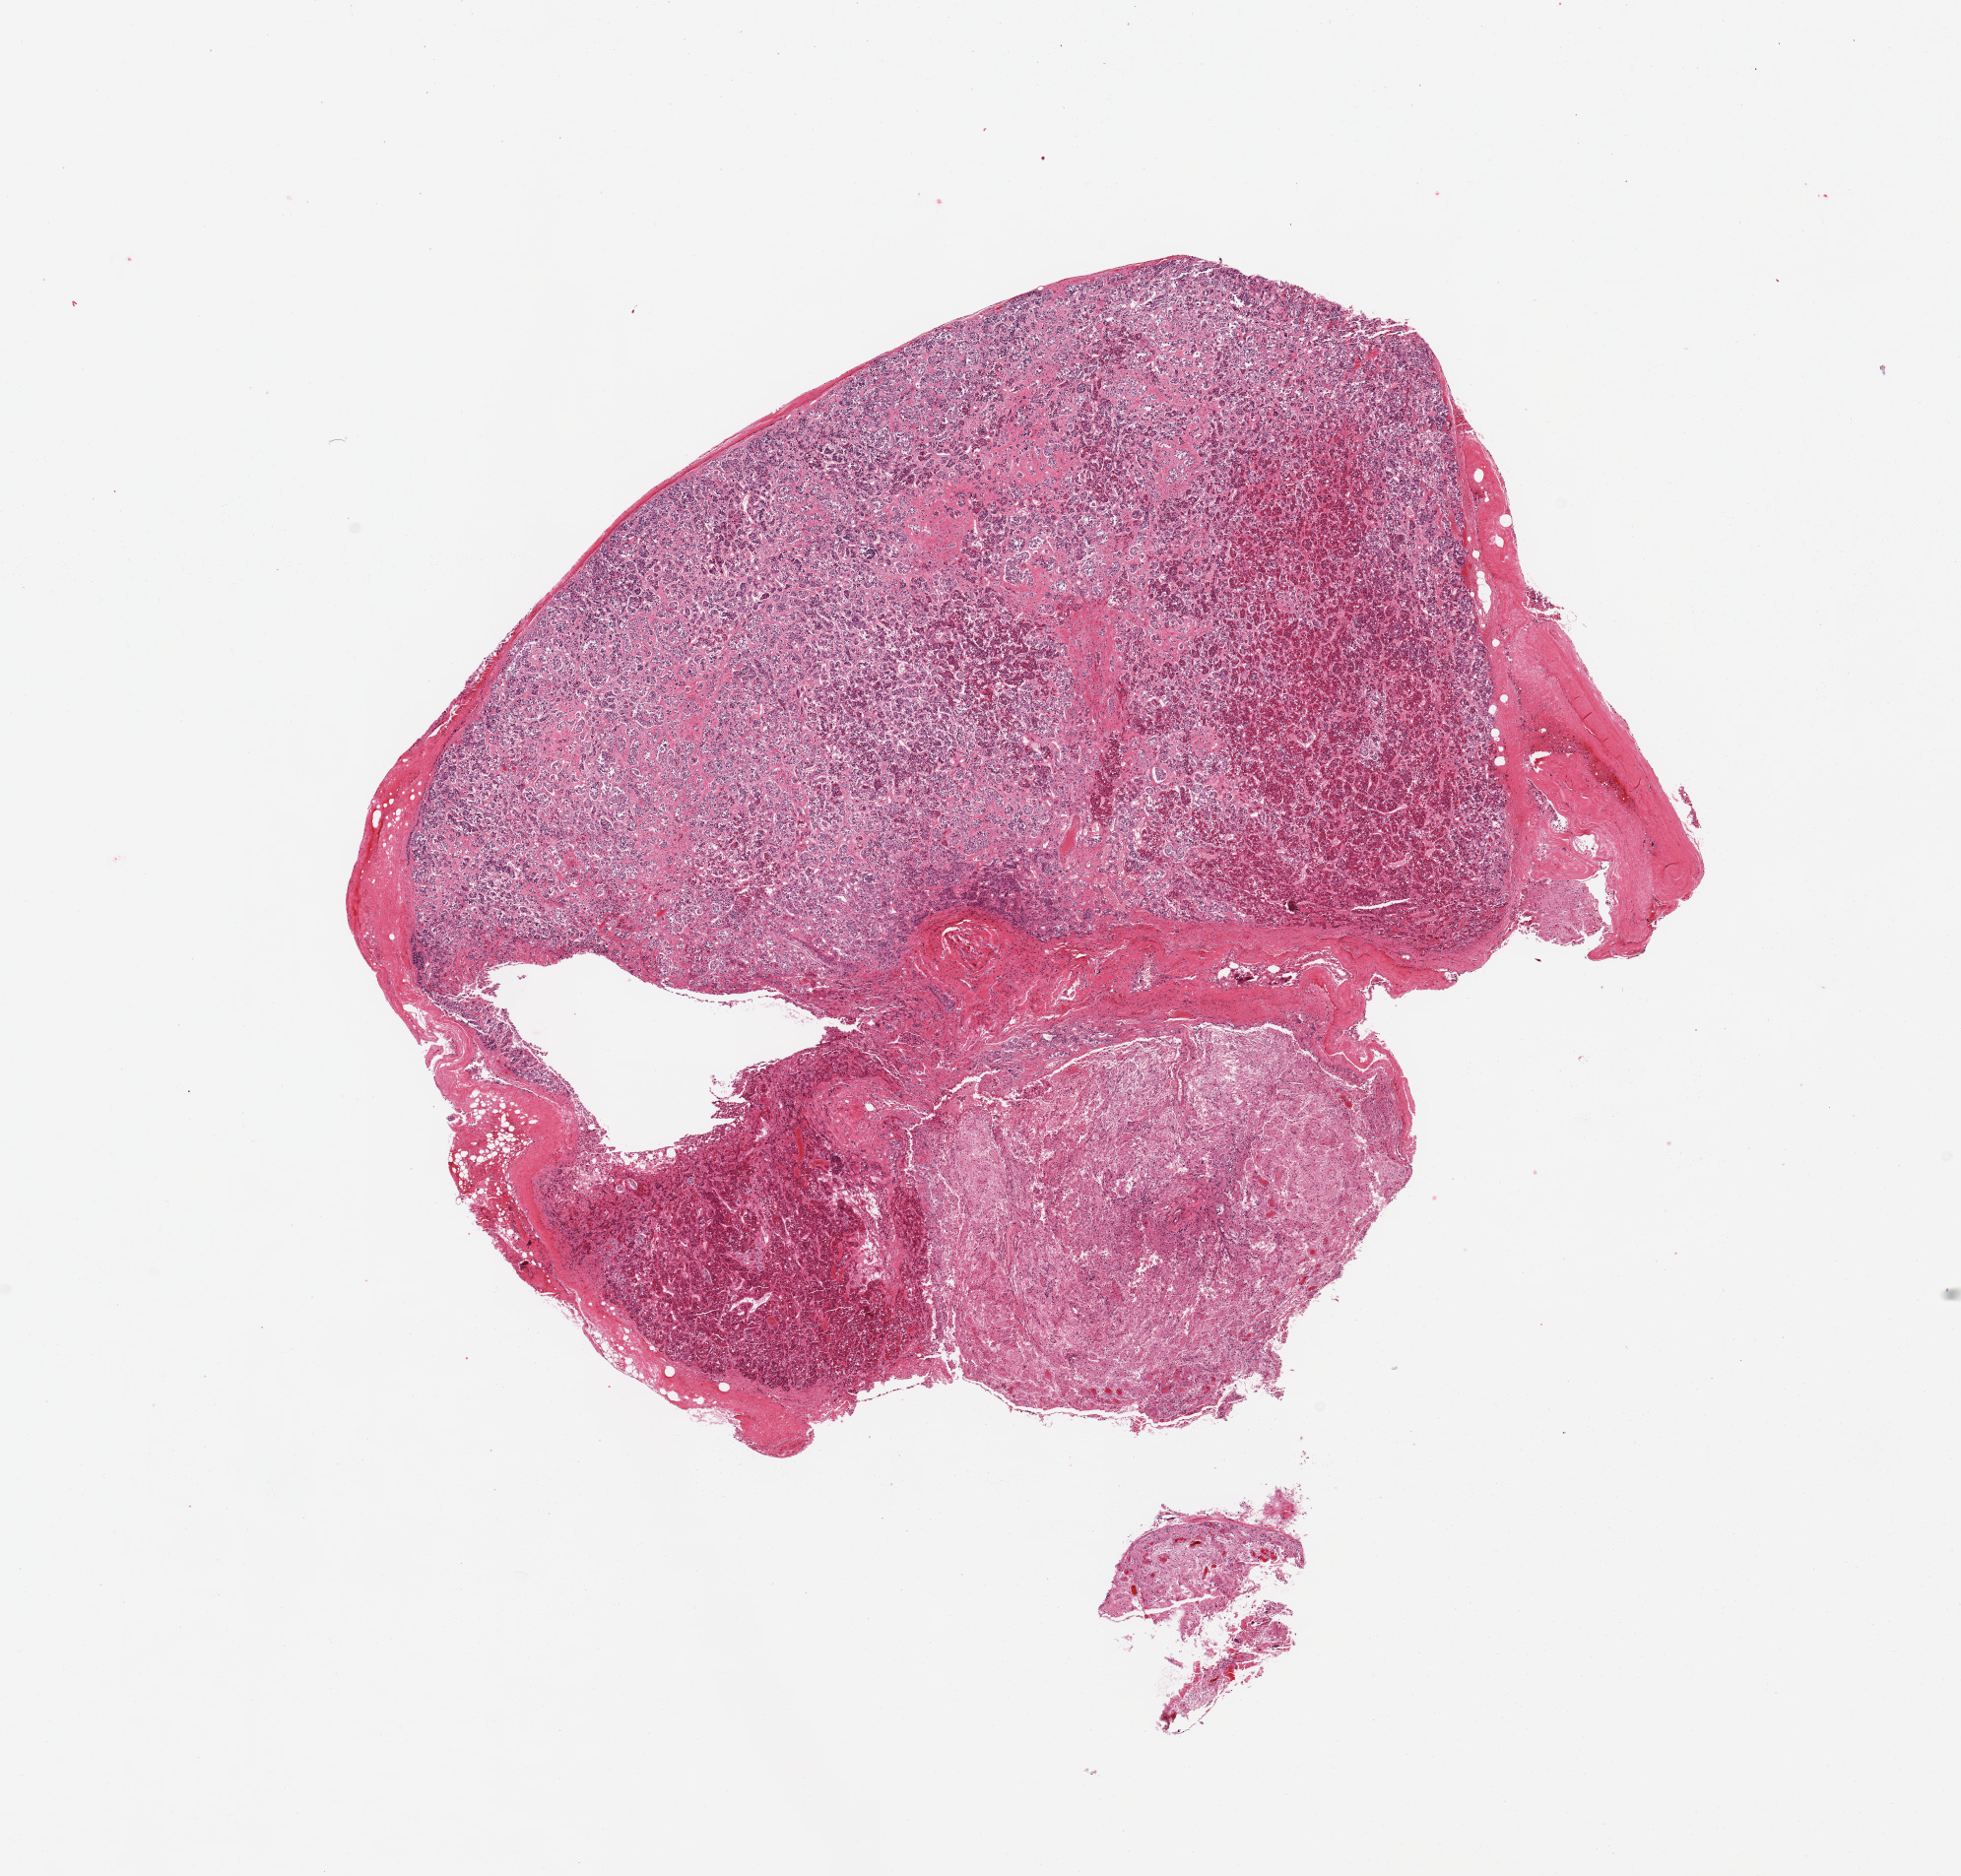
Hematoxylin and eosin (H&E) whole-slide image — shown as a low-resolution overview of the whole scanned area (about 15.8 x 15.1 mm, acquisition: 20x scan); PAXgene-fixed paraffin-embedded (PFPE) section; section of pituitary (target tissue); donor tissue sample. Donor: male.
Reviewer comment on this tissue sample: 1 piece; mainly adenohypophysis; ~3.5mm nodule of neurohypophysis.